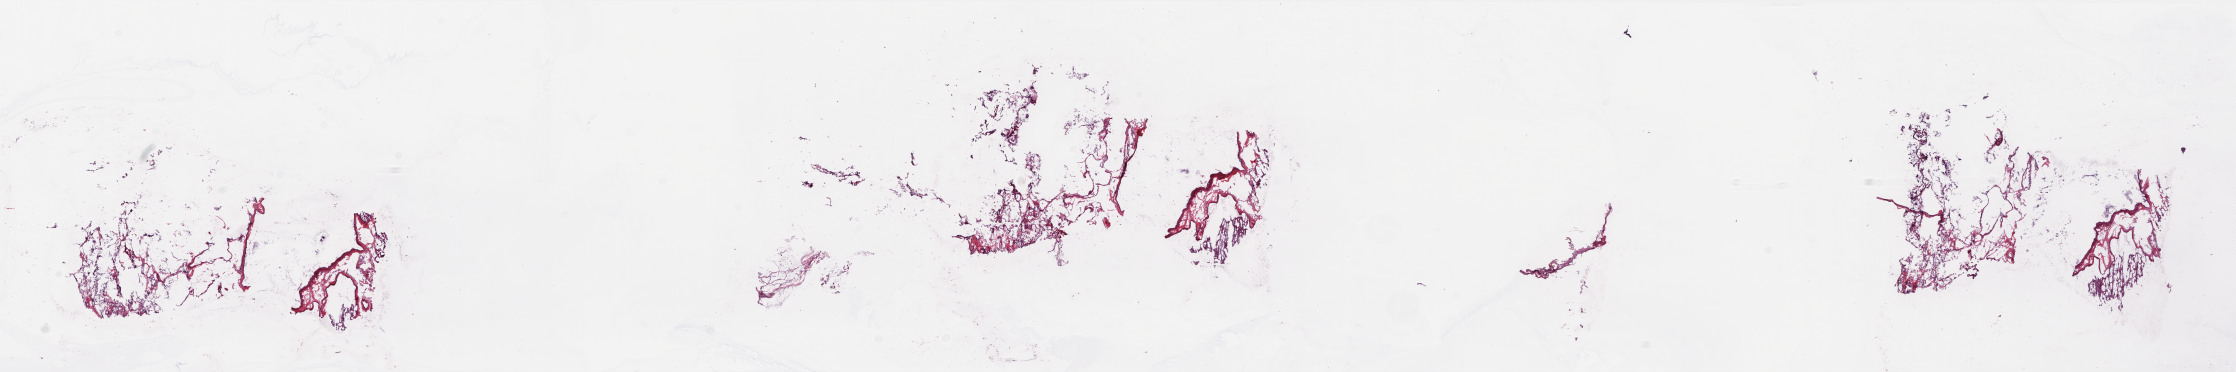
Hematoxylin and eosin (H&E) stained whole-slide image — whole scanned area (about 36.1 x 6.0 mm) shown as a low-resolution overview. Frozen section from the top of the tissue portion. Adrenal gland, solid tissue normal (non-tumour tissue) sample. Patient: female, age at initial diagnosis 19 years. Slide review estimates, as recorded: tumour cells 0%, tumour nuclei 0%, normal cells 100%, stromal cells 0%, necrosis 0%. Infiltration values recorded for this section: lymphocyte infiltration 0%, monocyte infiltration 0%, neutrophil infiltration 0%.
This section: solid tissue normal sample (biorepository sample class). Patient diagnosis: Medullary carcinoma, NOS (thyroid gland).